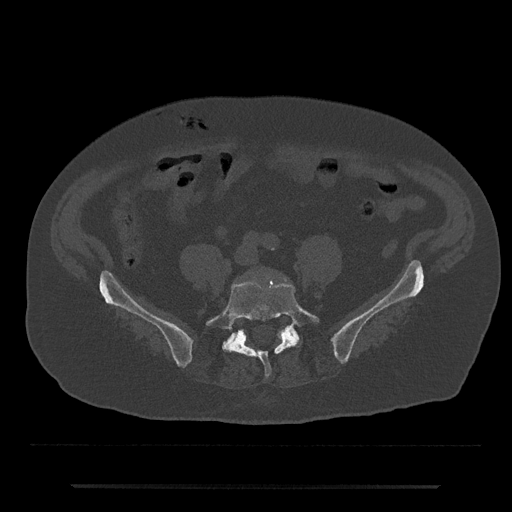
CT including the spine, one axial slice; position 287 of 797 along the scan axis; bone window (W 1800 / L 400 HU); 512 × 512 image matrix, field of view 434 × 434 mm. Male patient, age 80 years. From the clinical record (not read from this slice): primary cancer: prostate.
Structures marked on this image (semi-automatically segmented with operator editing):
- L5 vertebra: box from (x=206, y=282) to (x=320, y=377) px